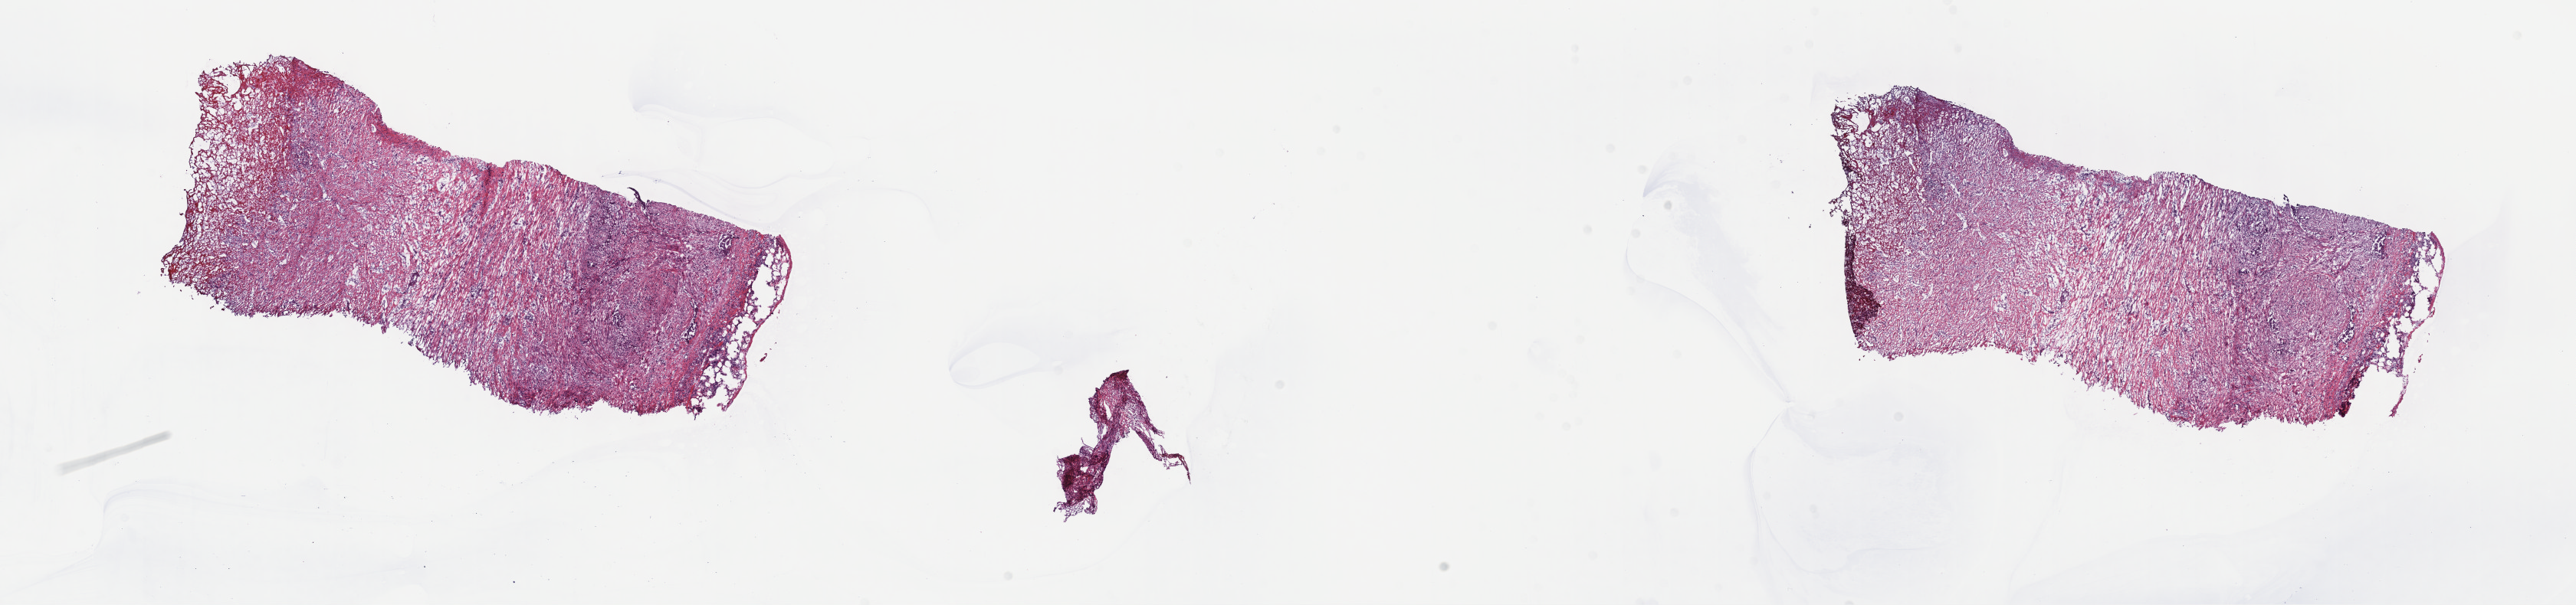
Digitized H&E-stained tissue section (whole slide) — shown as a low-resolution overview of the whole scanned area (about 27.2 x 6.4 mm, slide scanned at 40x), frozen section from the top of the tissue portion, primary tumour sample from the mesothelium. Male, age 71 years at initial diagnosis. Composition of this section per pathologist review: tumour cells 100%, tumour nuclei 80%.
Histologic diagnosis: Mesothelioma, biphasic, malignant (pleura, NOS).